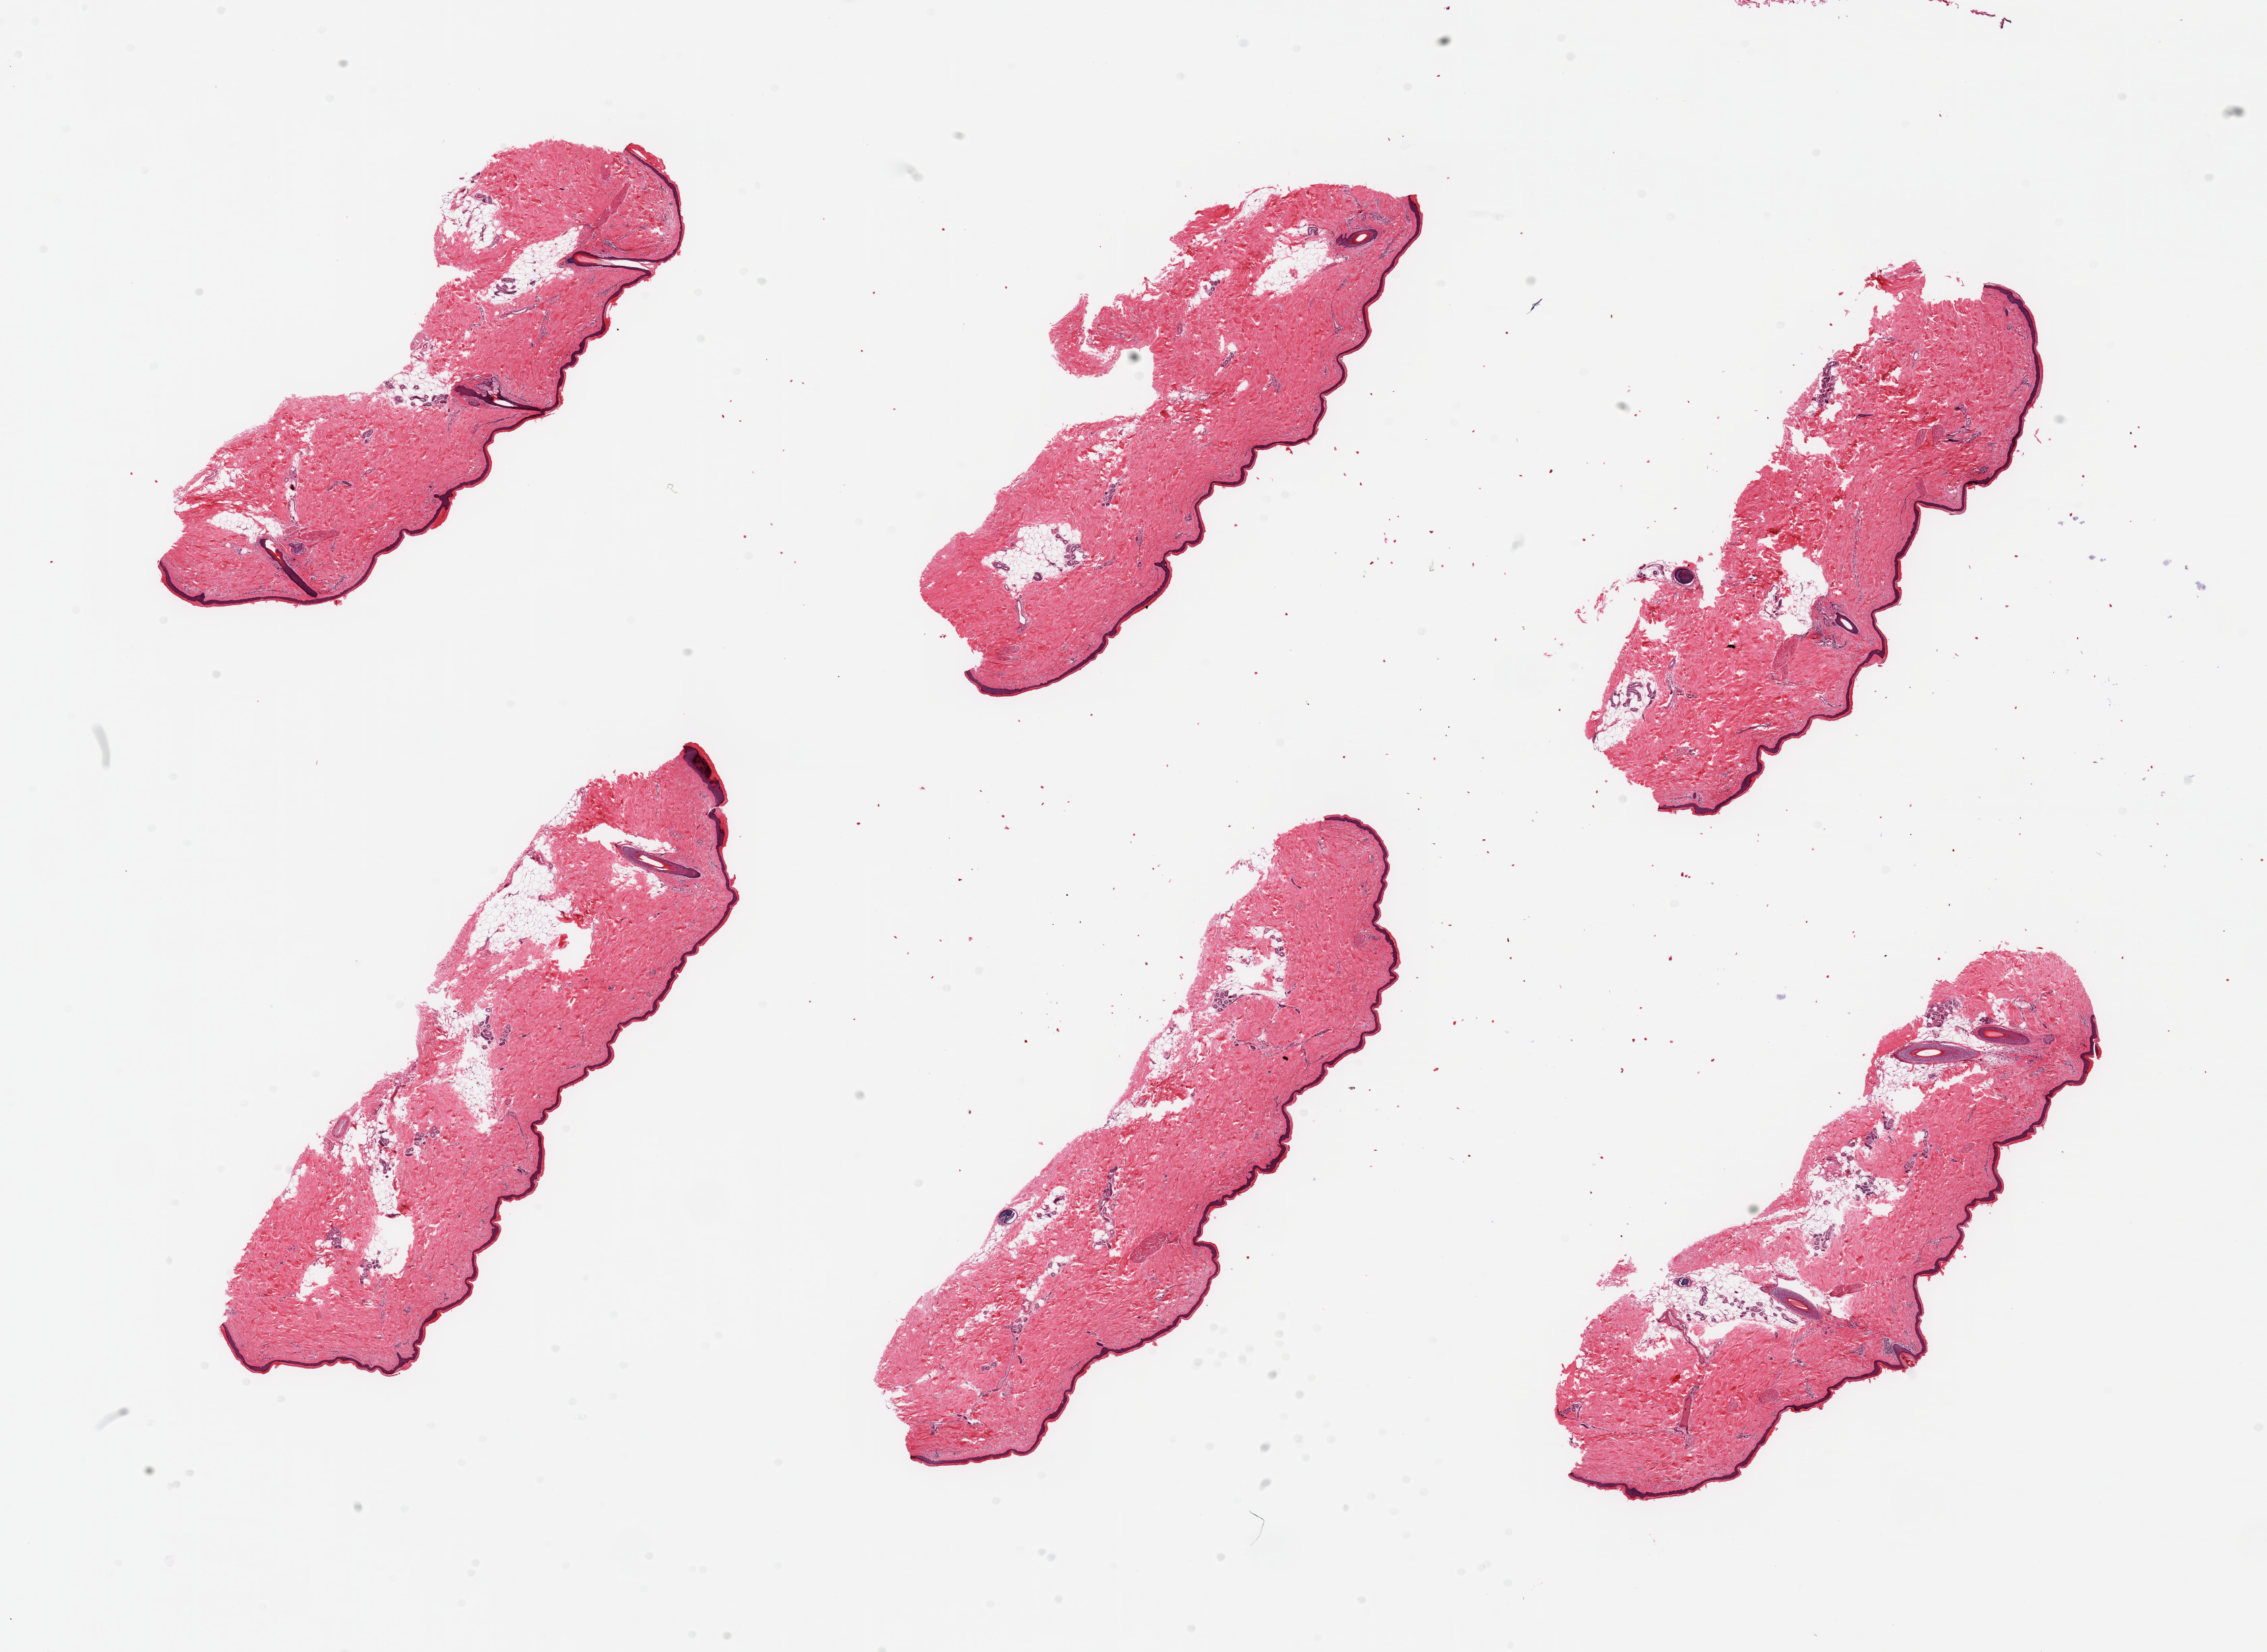
Digitized H&E-stained section, whole scanned area (about 26.6 x 19.4 mm, acquisition: 20x scan) shown as a low-resolution overview; PAXgene-fixed paraffin-embedded (PFPE) section; section of skin of lower leg (target tissue); tissue donor sample.
* pathologist's review note for this sample: 6 pieces; includes up to ~20% internal fat, epidermis measures 37 microns